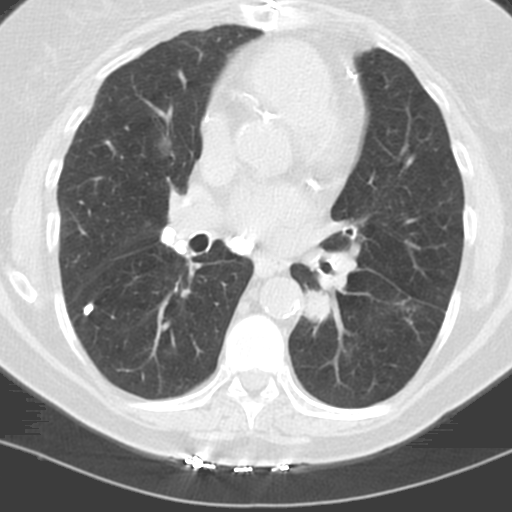
Axial slice from a low-dose chest CT screening exam. First (baseline) screen. Lung window (W 1500 / L -600 HU). 3.2 mm slice thickness. Standard (soft-tissue) reconstruction kernel (C). 120 kVp. Slice 65 of 121 in the series. Female participant, aged 60 years at enrolment. Former smoker at enrolment.
- Lesion marked by an expert reader, bounding box <292,281,340,332> (left, top, right, bottom; pixels).
- The screening reader recorded 3 non-calcified nodules or masses ≥4 mm on this exam (left lower lobe, left lower lobe, right middle lobe); which of them this box marks is not recorded.
- Later outcome: lung cancer diagnosed 96 days after this screen — adenocarcinoma, NOS, left lower lobe, stage IV (AJCC 6th edition), 22 mm at pathology.